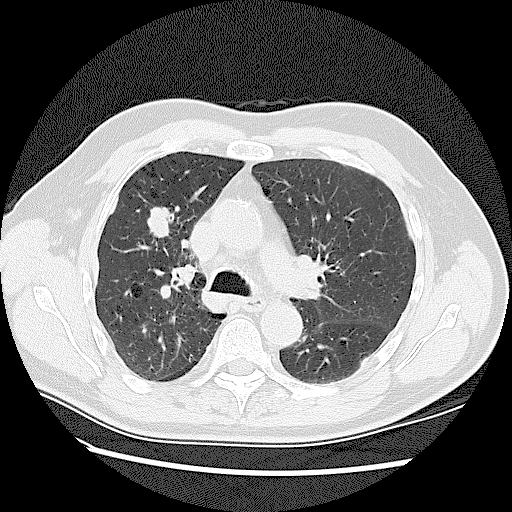
Axial slice from a low-dose chest CT screening exam, first (baseline) screen, lung window (W 1500 / L -600 HU), lung (sharp) reconstruction kernel (LUNG), 120 kVp, slice 46 of 128 in the series, 512 × 512 image matrix. Male, age 72 years at enrolment. Current smoker at enrolment.
• Expert-annotated lung lesion, bounding box (x1, y1, x2, y2) in pixels: (133, 201, 181, 240).
• The screening reader recorded 2 non-calcified nodules or masses ≥4 mm on this exam; which of them this box marks is not recorded.
• Official screen result: positive, change unspecified: nodule(s) >= 4 mm or enlarging nodule(s), mass(es), or other non-specific abnormalities suspicious for lung cancer.
• Later outcome: lung cancer diagnosed 42 days after this screen — adenocarcinoma, NOS, right upper lobe, stage IV (AJCC 6th edition), 45 mm at pathology.